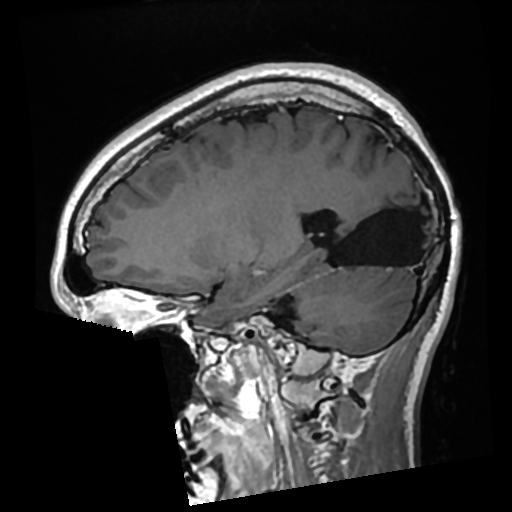
Brain MRI from a brain-tumour surgery series, one sagittal slice. Position 107 of 276 along the scan axis. T1-weighted post-contrast. 512 × 512 image matrix. Case-level facts recorded for this patient, not image findings: histopathology: Glioma with ependymal features; WHO grade: 2; tumour location: Left Parietal.
Annotated regions visible in this slice (manually delineated by an expert):
- previous resection cavity: bounding box [x1, y1, x2, y2] px = [327, 186, 422, 266]